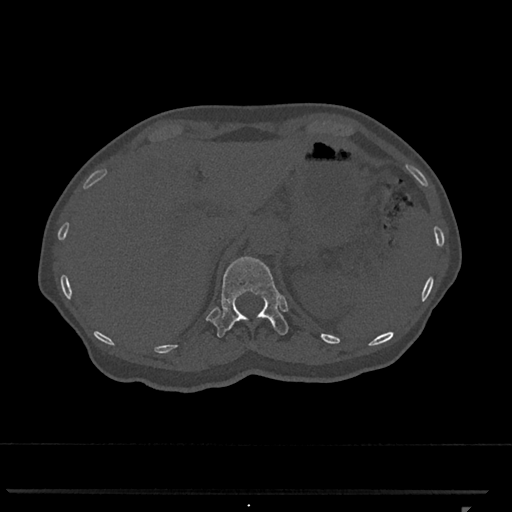
CT including the spine, one axial slice. Position 470 of 793 along the scan axis. Bone window (W 1800 / L 400 HU). 512 × 512 image matrix, field of view 380 × 380 mm. Female patient, age 62 years. Case-level facts recorded for this patient, not image findings: primary cancer: renal.
Structures marked on this image (semi-automatically segmented with operator editing):
- T12 vertebra: bounding box (x1, y1, x2, y2) in pixels: (213, 256, 289, 338)